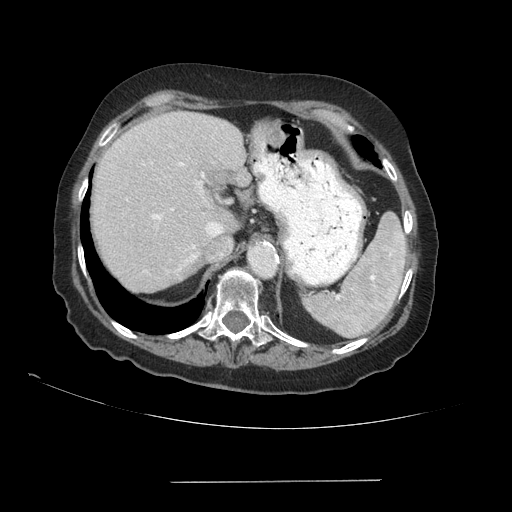
Contrast-enhanced abdominal CT (liver protocol), one axial slice; reconstruction kernel STANDARD; 140 kVp; soft-tissue window (W 400 / L 40 HU); 512 × 512 image matrix. From the clinical record (not read from this slice): diagnosis: hepatocellular carcinoma (patient treated with transarterial chemoembolisation; whether this scan precedes or follows treatment is not stated here); TNM stage (as recorded): Stage-IVA; Child-Pugh class: A; tumour differentiation: poorly differentiated.
Structures marked on this image (semi-automatically segmented with operator editing):
- liver parenchyma outside the tumour (the mass and vessels are separate outlines, so this box may not span the whole liver): bounding box [x1, y1, x2, y2] px = [92, 110, 244, 292]
- liver vessels: [152, 162, 211, 261]